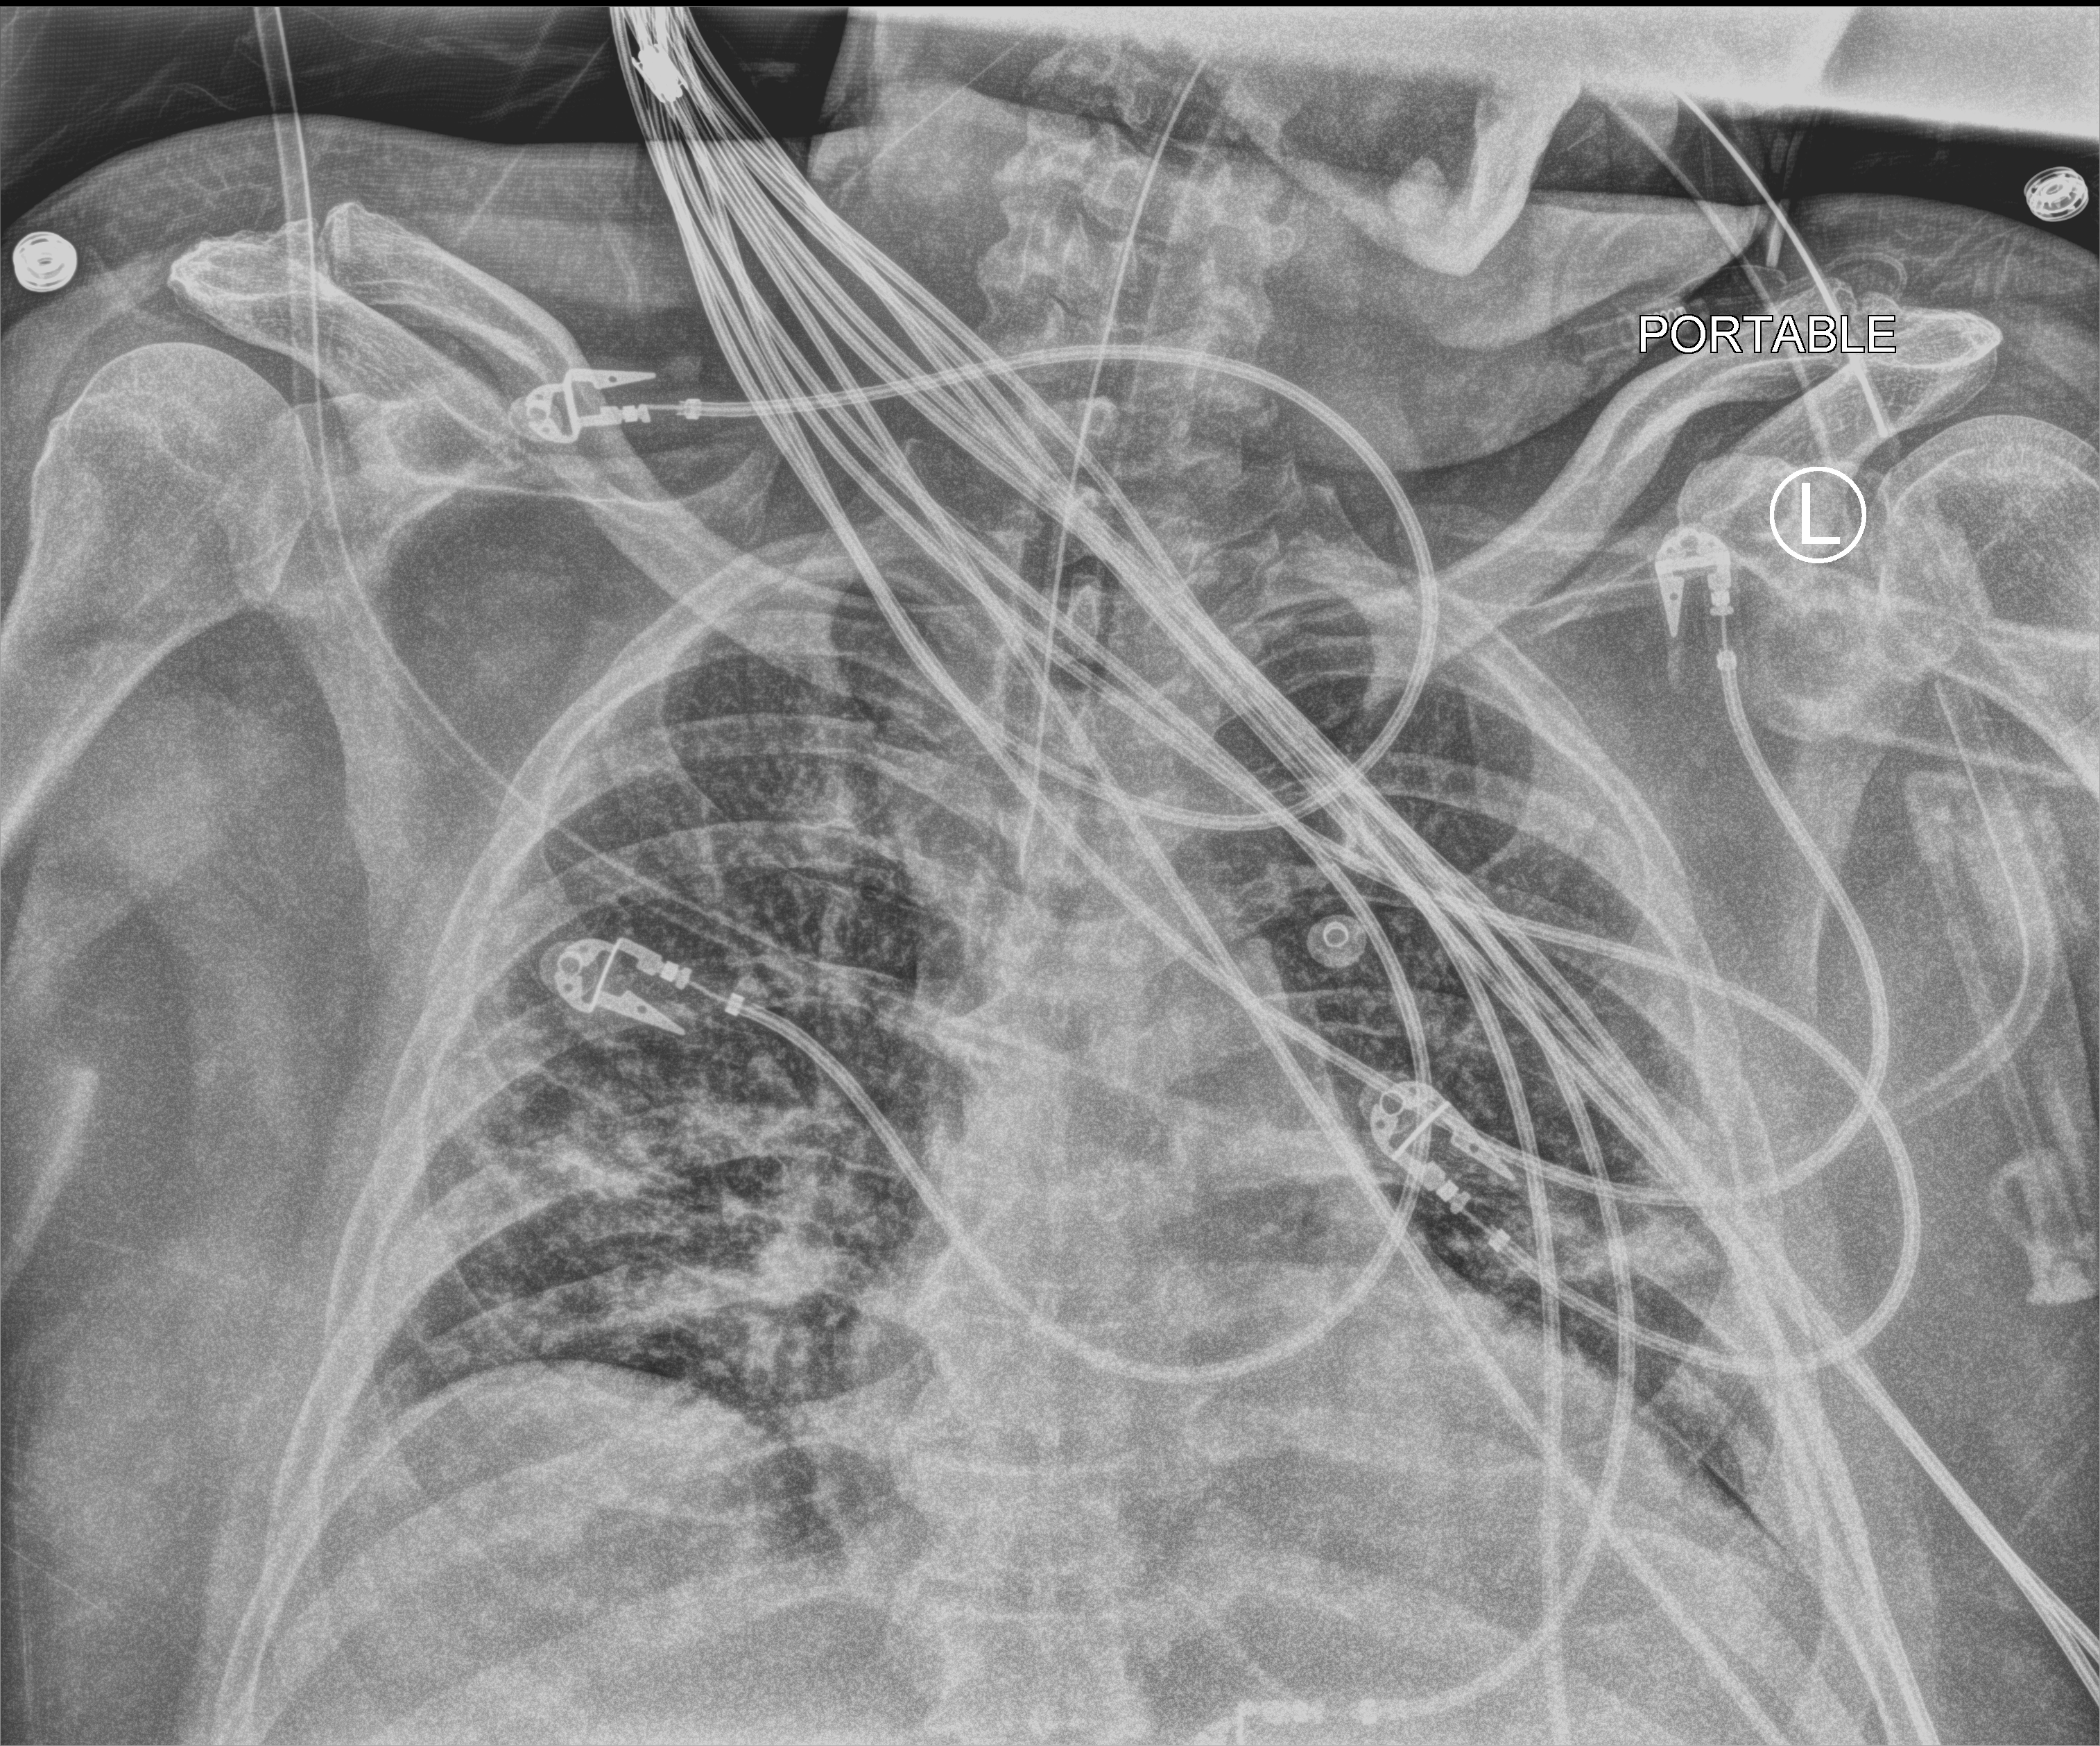
Bedside chest radiograph (computed radiography), anteroposterior (AP) projection. Patient hospitalised with COVID-19; male, aged 18–59 years.
Admission-level facts for this patient (not findings on this image; timing relative to this image not recorded): mechanically ventilated during this hospital stay: yes; length of hospital stay: 21 days.